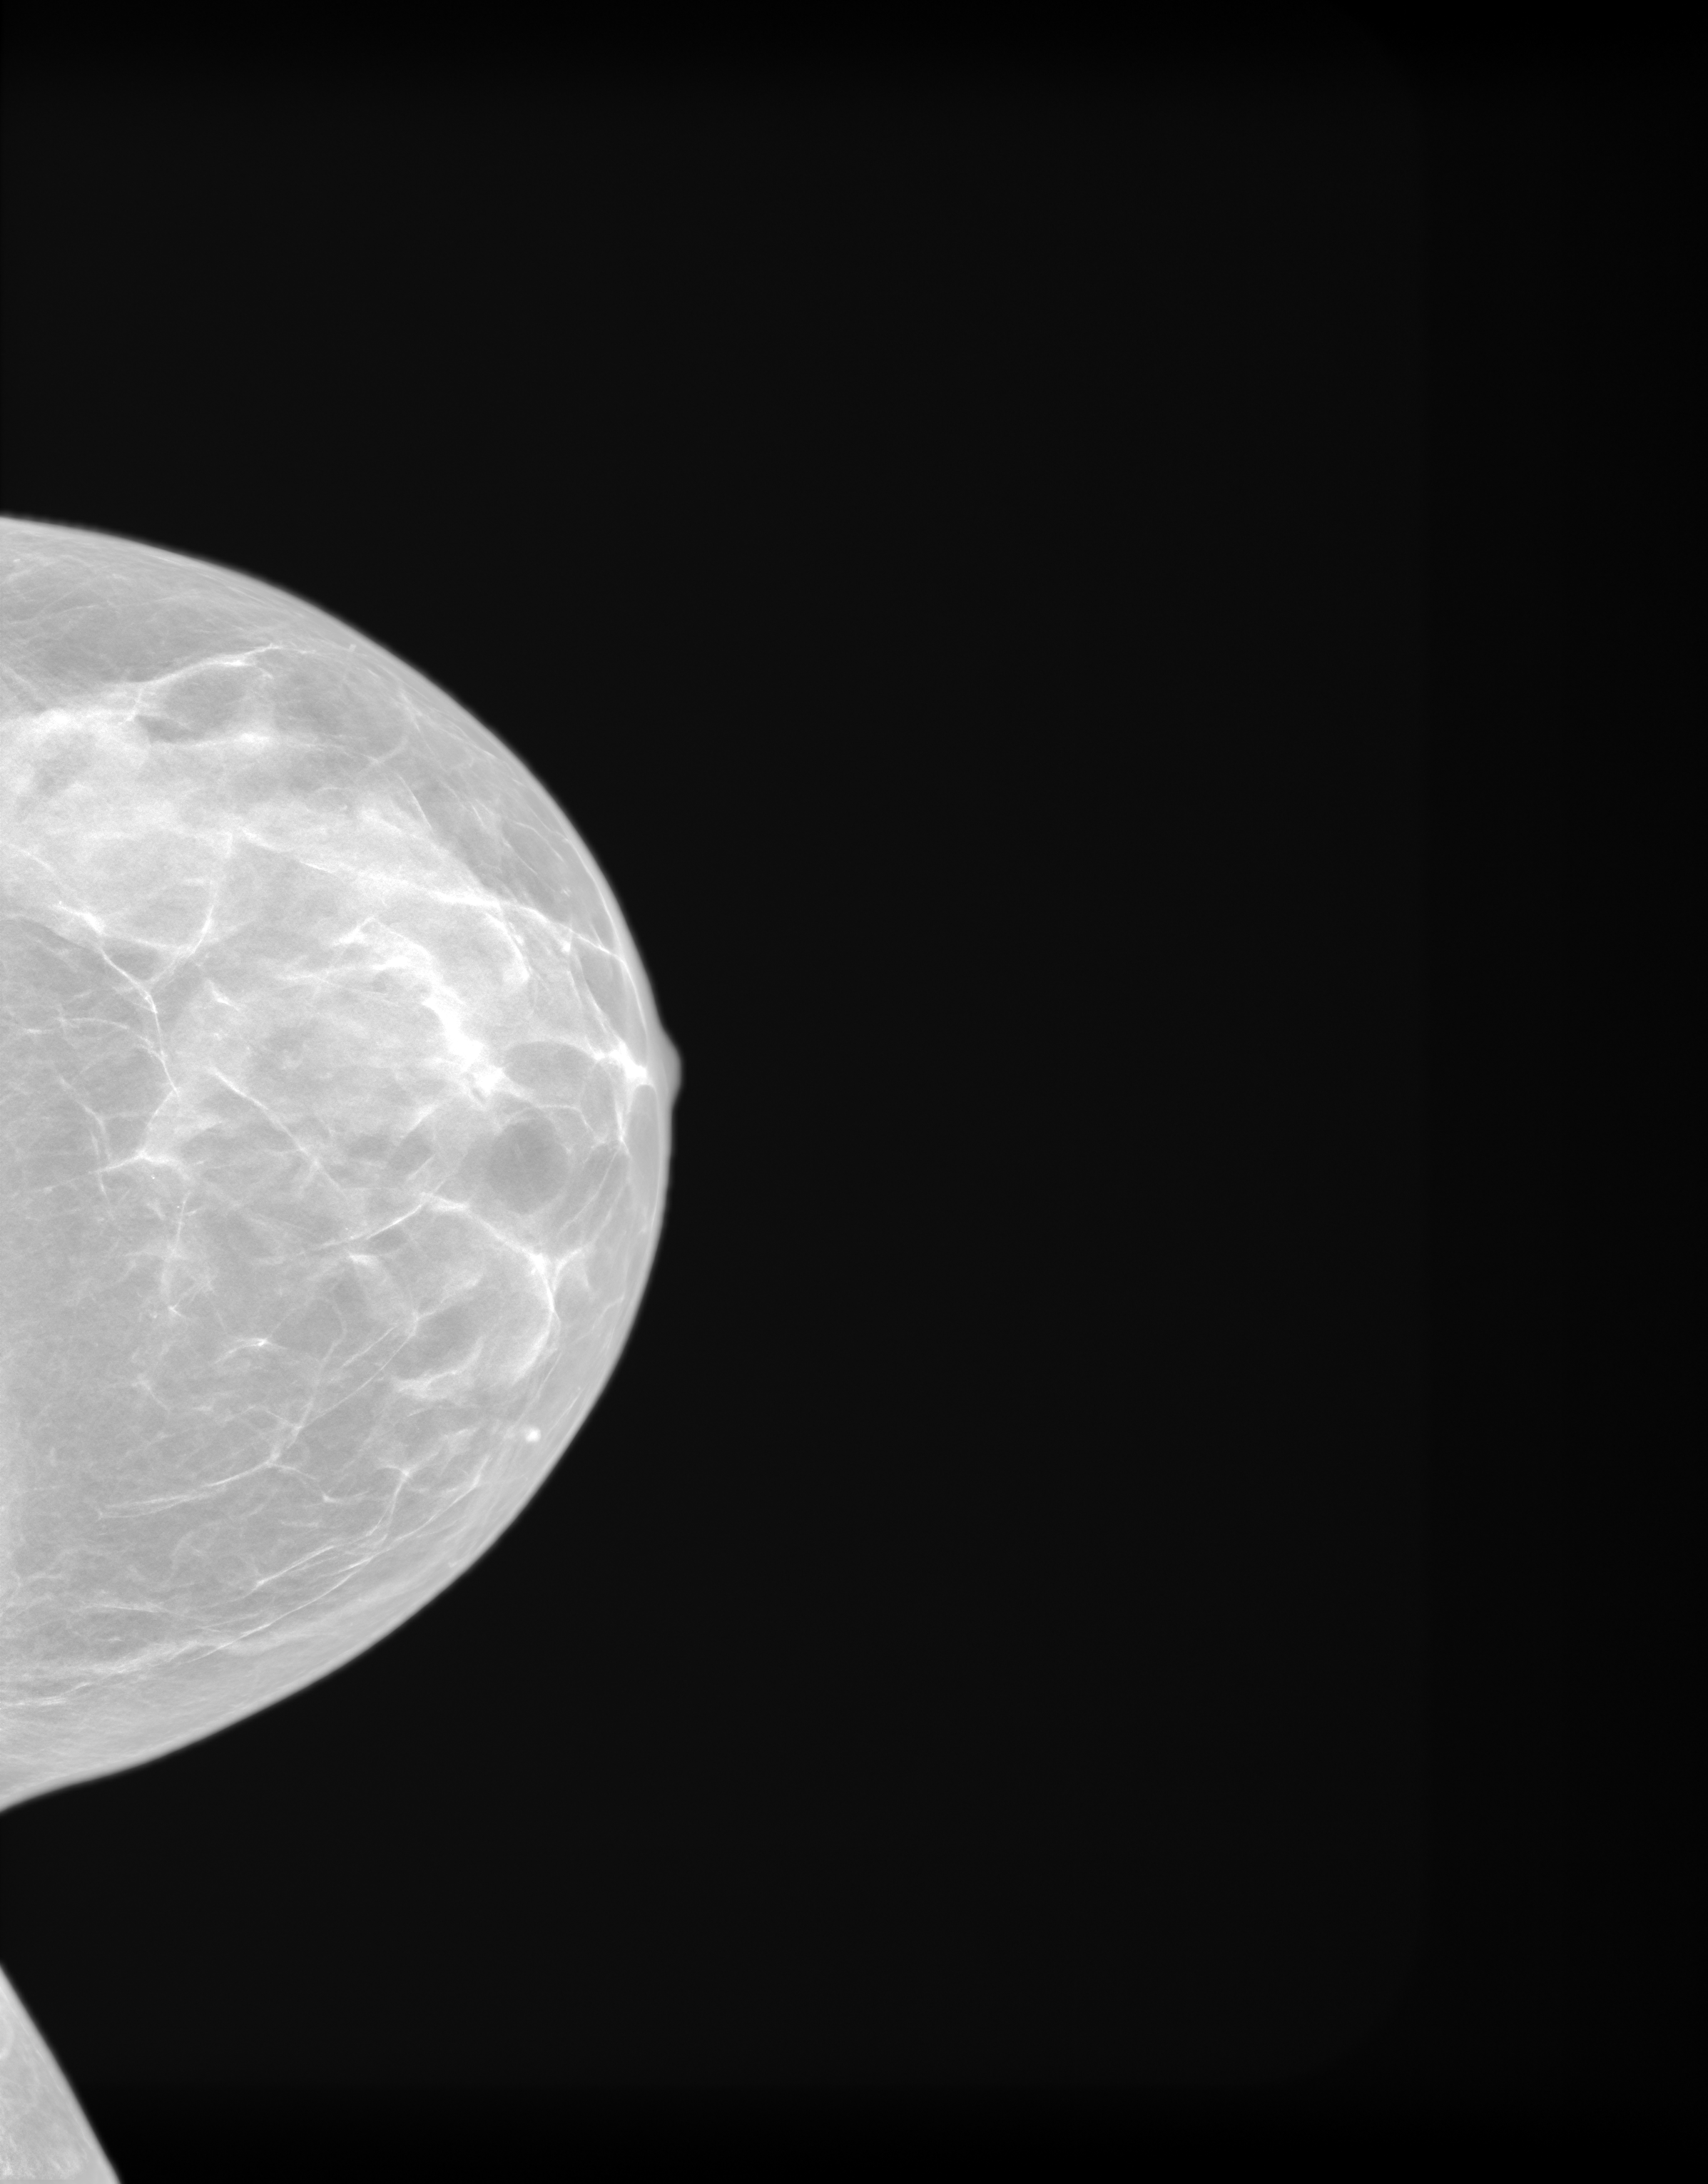
Synthesized 2-D mammogram reconstructed from digital breast tomosynthesis; left breast; CC view; annual screening mammography examination. Patient aged 51 years (female).
BI-RADS breast density category at the screening exam (both breasts, scale 1–4): 3. Final BI-RADS assessment for this screening round (tomosynthesis exam, both breasts): category 1. Recall: no recall after this screen.